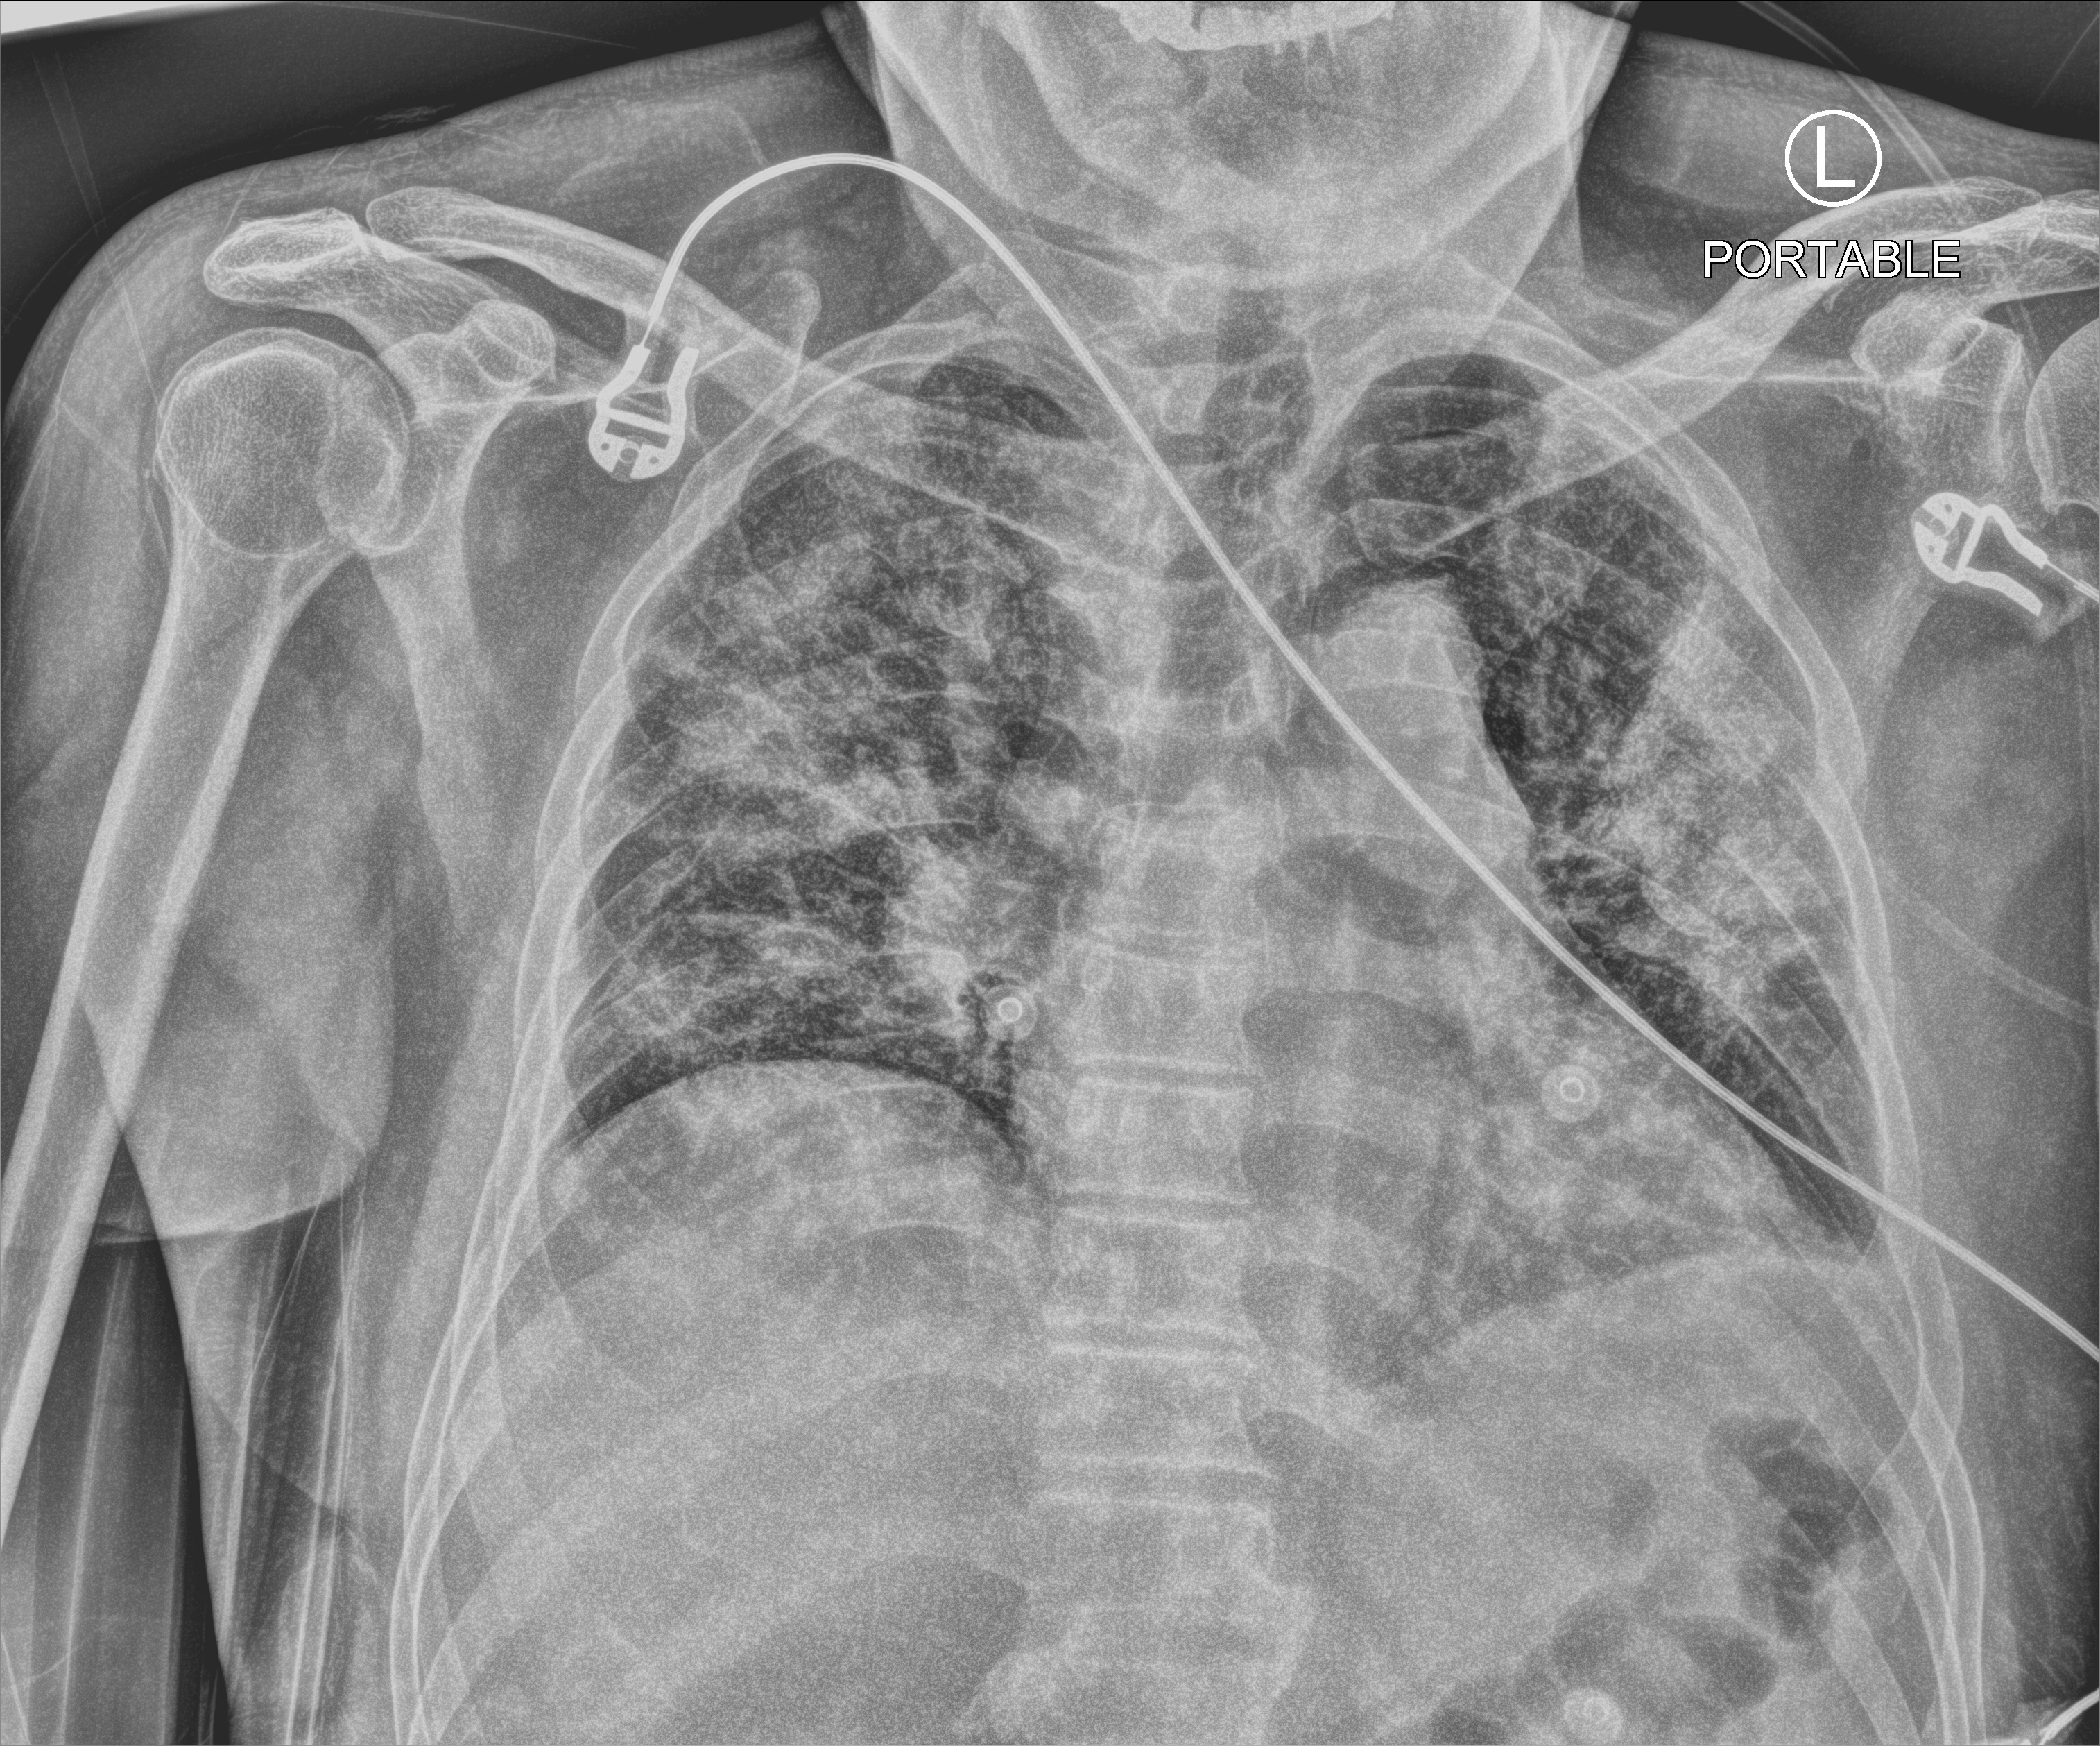
Portable chest radiograph; anteroposterior (AP) projection. Male patient hospitalised with COVID-19, age 60–74 years.
Hospital-stay facts (about this admission, not read from this image; timing relative to this image not recorded):
- diabetes (admission record): yes
- length of hospital stay: 14 days
- admitted to intensive care during this hospital stay: yes